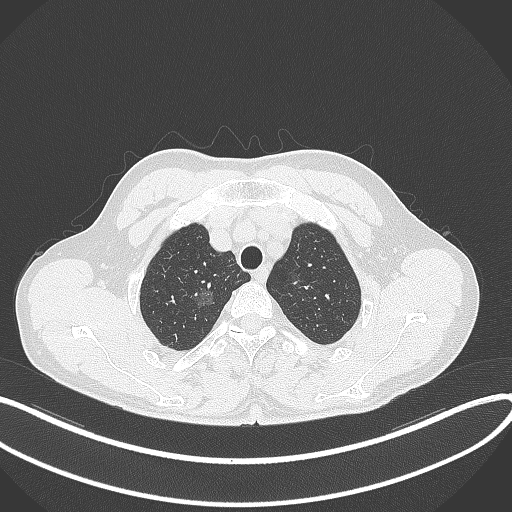
Chest CT, one axial slice; slice 321 of 407 in the series (ordered by position); 120 kVp; lung window (W 1500 / L -600 HU); 1 mm slice thickness; 512 × 512 image matrix. Patient: male, 58 years. From the clinical record (not read from this slice): clinical TNM (as recorded): T1c N0 M0; histopathological grade: G1-2.
Annotated regions visible in this slice (bounding box drawn by a radiologist):
- lung tumour (recorded histology: adenocarcinoma): bounding box <190,280,217,312> (left, top, right, bottom; pixels)